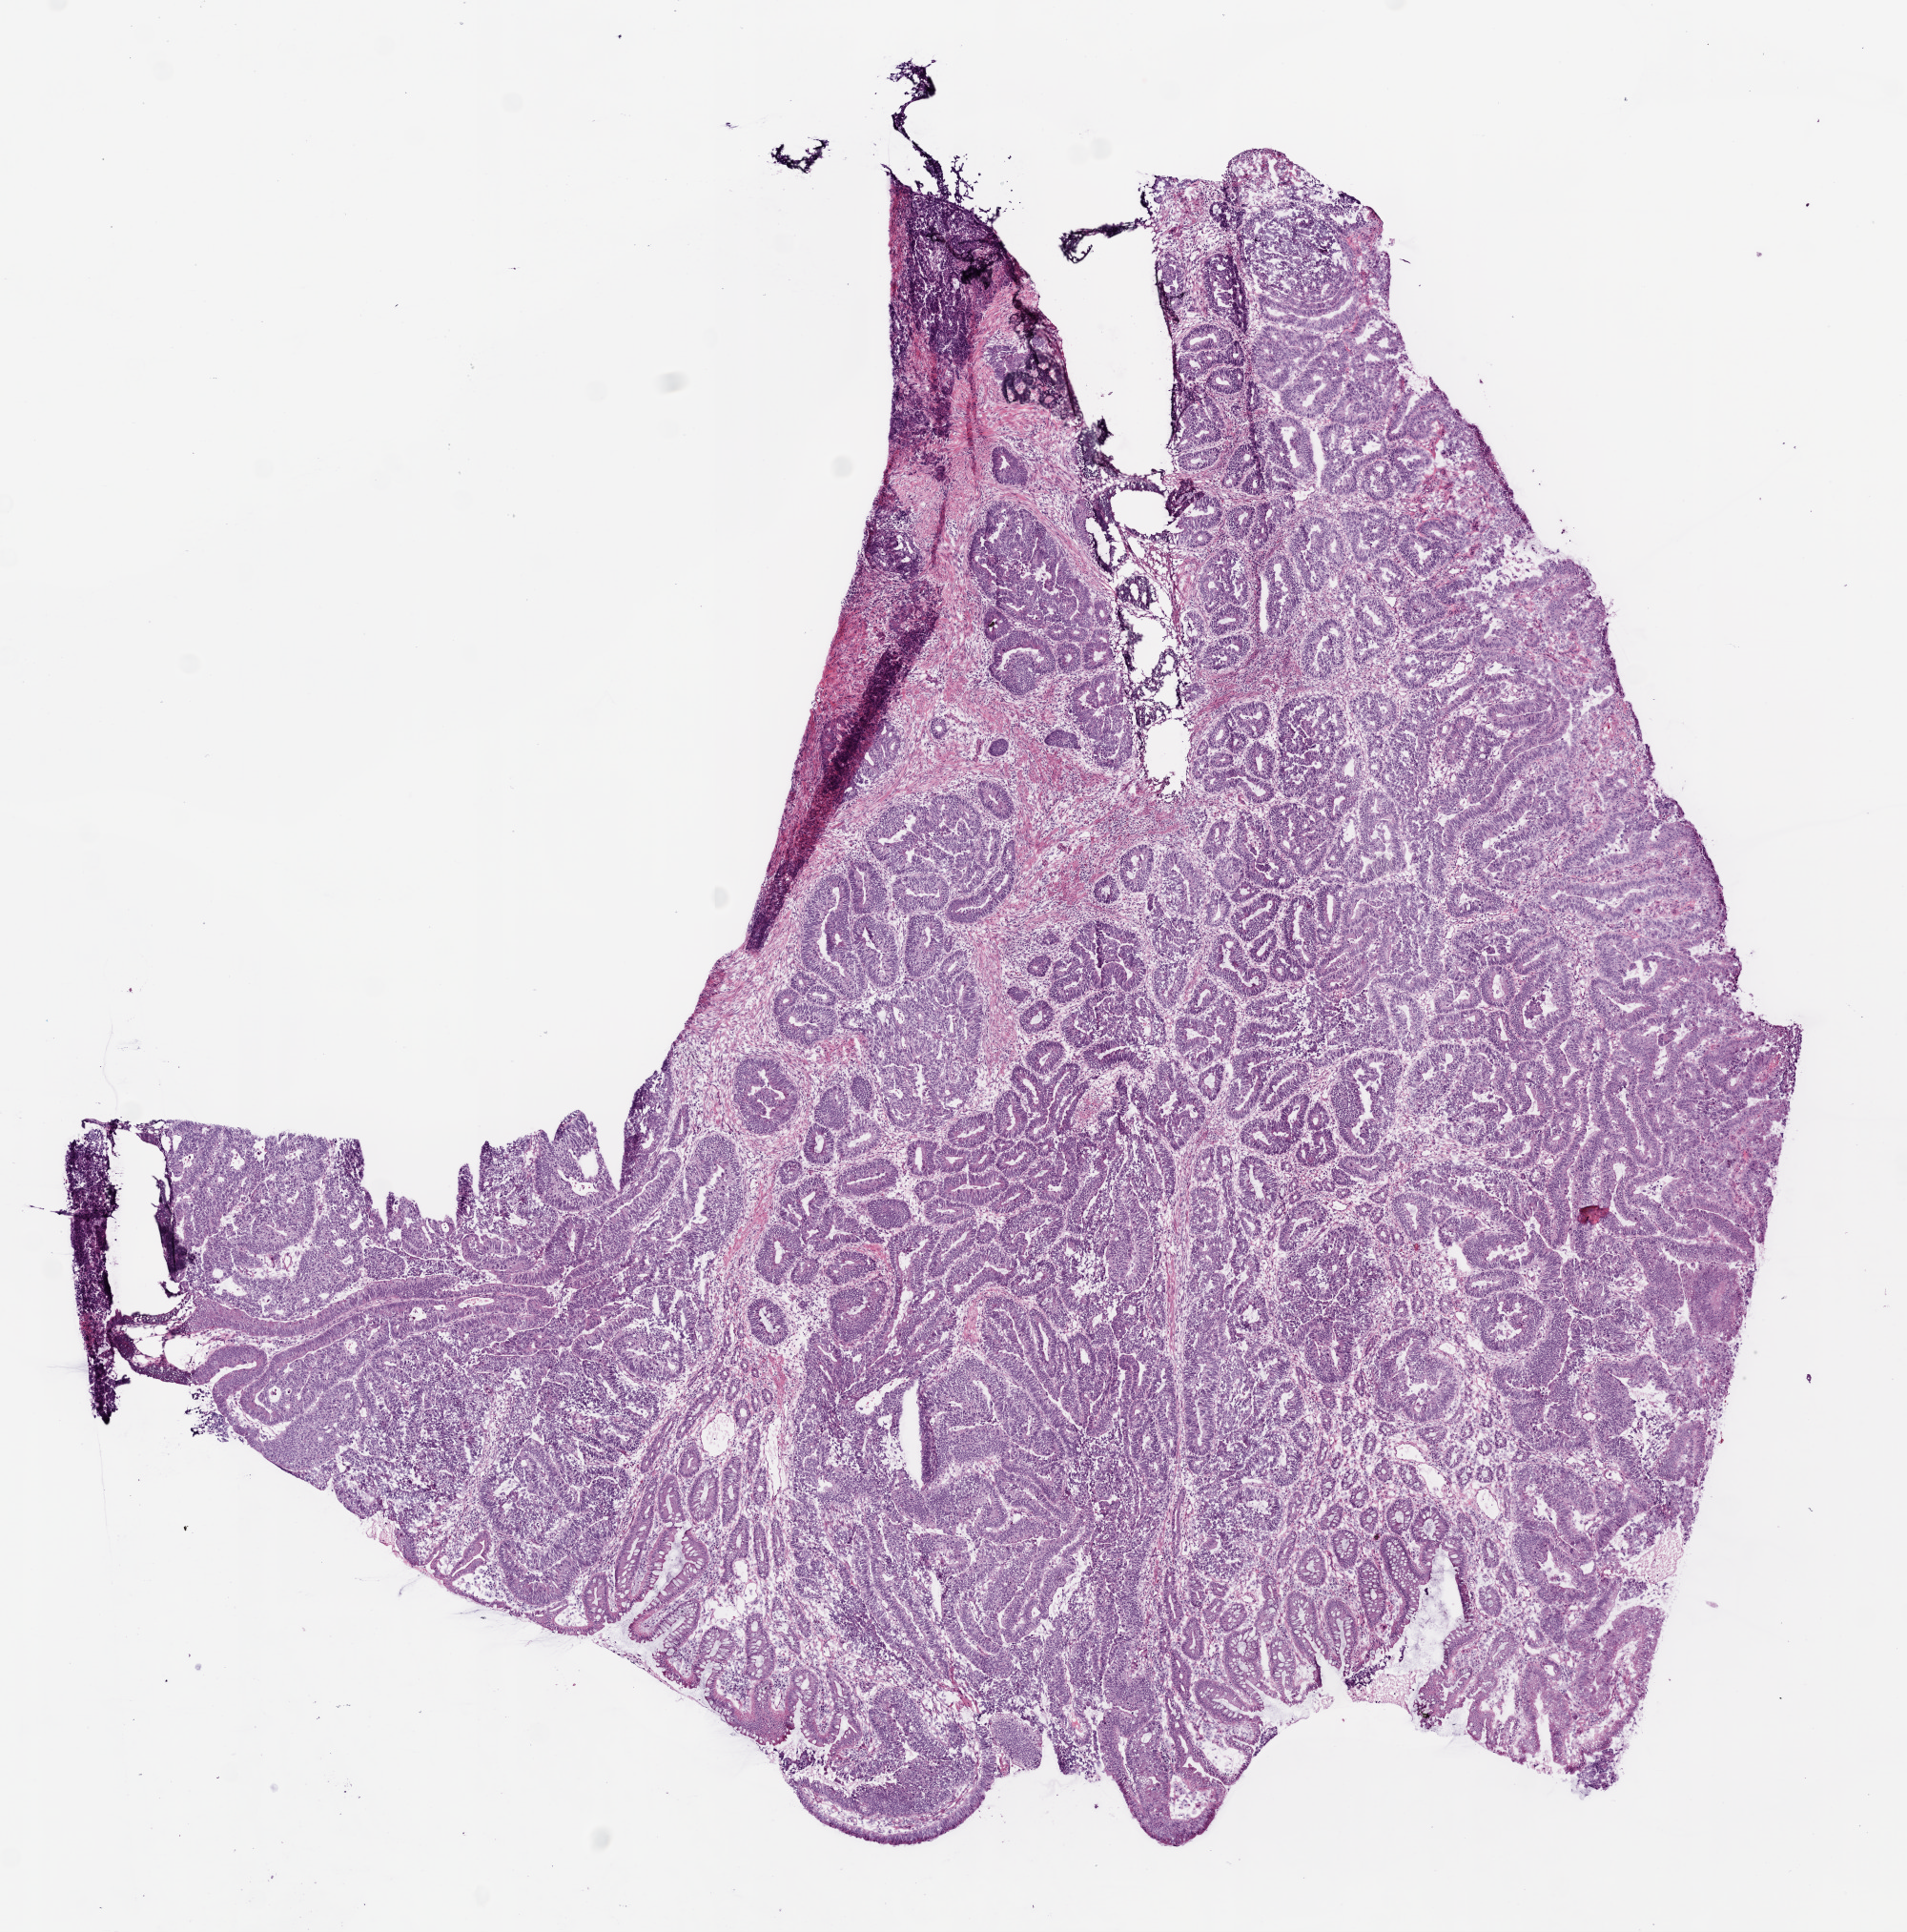
Whole-slide histology image, H&E — shown as a low-resolution overview of the whole scanned area (about 8.0 x 8.1 mm); frozen section; sample: primary tumour, colon. Male, age 38 years at initial diagnosis. Slide review estimates, as recorded: tumour cells 80%, tumour nuclei 80%, normal cells 5%, stromal cells 14%, necrosis 1%.
* AJCC pathologic stage: IIIB (7th edition)
* pathologic diagnosis: Adenocarcinoma, NOS